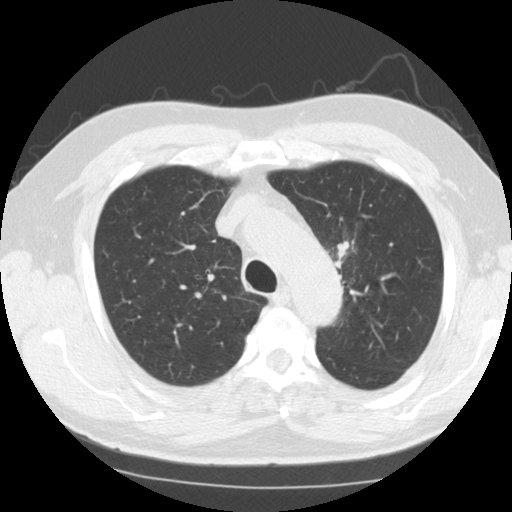
Chest CT (low-dose screening protocol), one axial image, third screening round (two years after baseline), lung window (W 1500 / L -600 HU), 2.5 mm slice thickness, slice 29 of 124 in the series. Male, age 60 years at enrolment. Current smoker at enrolment.
Expert reader's lesion annotation, bounding box <319,230,371,293> (left, top, right, bottom; pixels). Screening reader's record for this exam (one nodule recorded; not confirmed to be the boxed lesion): non-calcified nodule or mass ≥4 mm, left upper lobe, 24 × 21 mm, smooth margins, soft tissue attenuation, pre-existing on the prior screen: no. Participant outcome: lung cancer diagnosed 14 days after this screen — small cell carcinoma, NOS, left upper lobe, stage IIA (AJCC 6th edition), 26 mm at pathology.